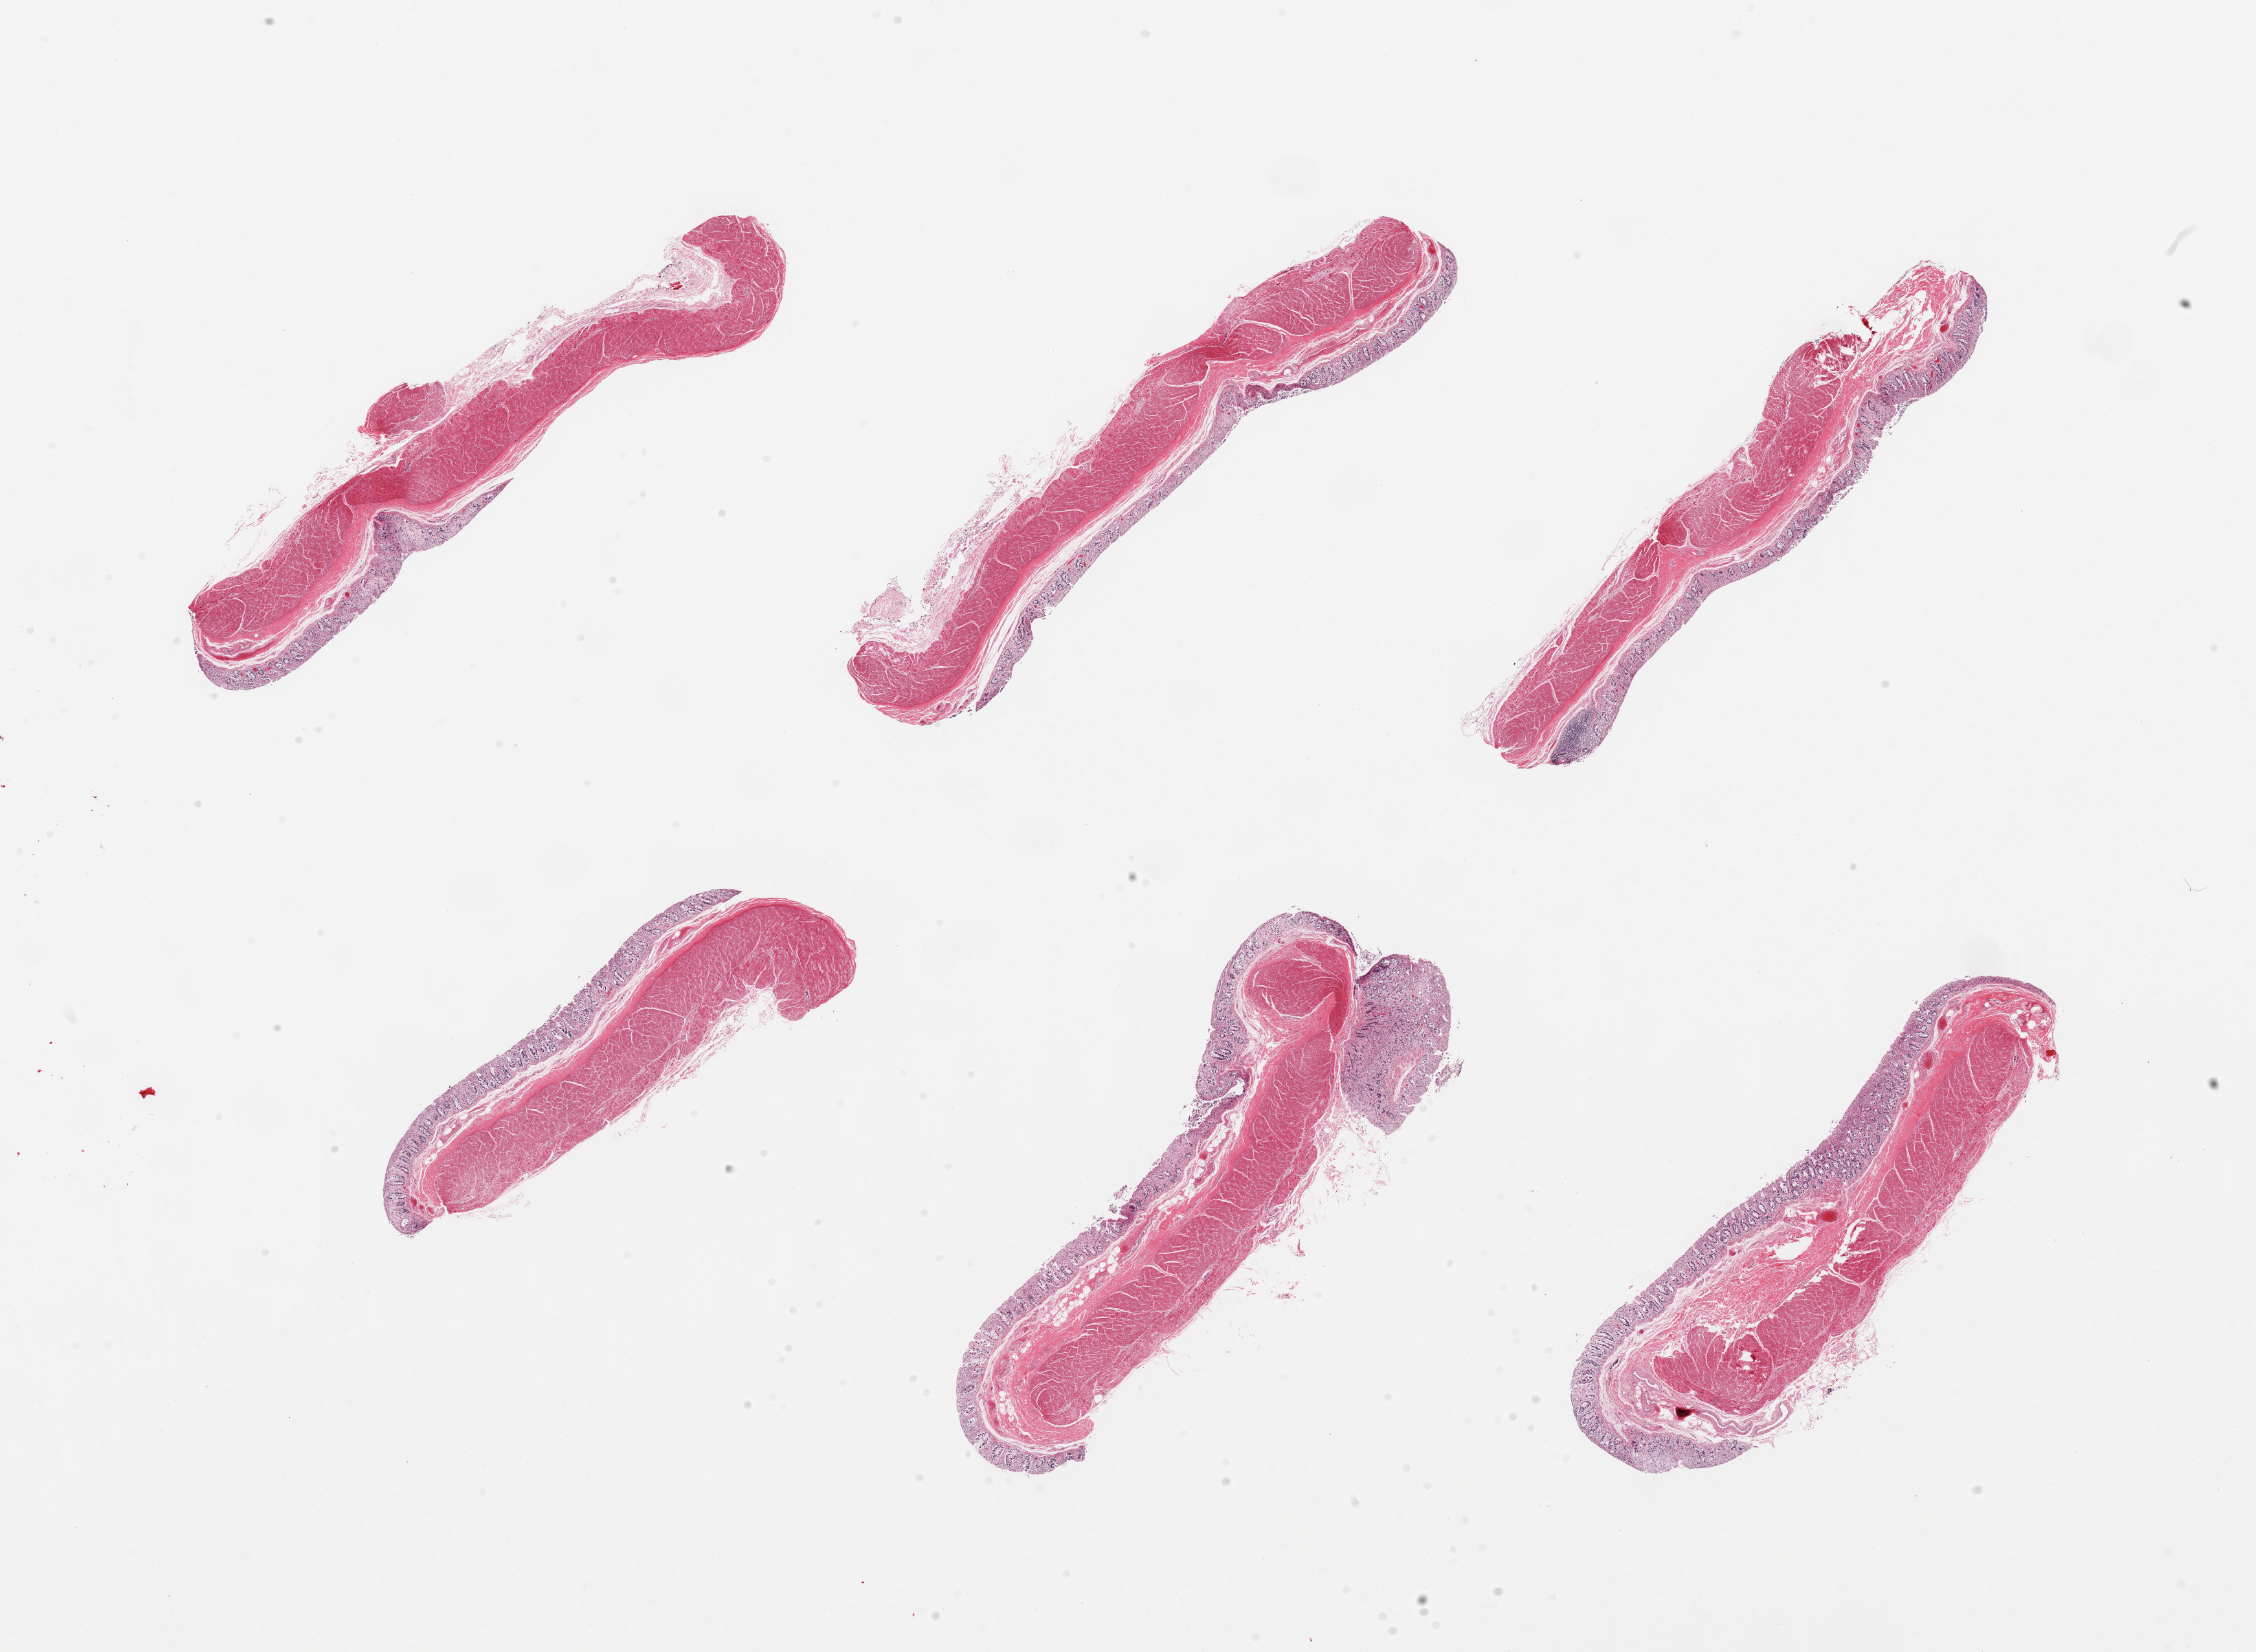
Digitized hematoxylin and eosin (H&E)-stained section — whole scanned area (about 27.6 x 20.2 mm) shown as a low-resolution overview. PAXgene-fixed paraffin-embedded (PFPE) section. Sampled site (target tissue): transverse colon. Tissue donor sample. Female donor.
- pathologist's review note for this sample: 6 pieces, severely autolyzed mucosa and muscularis